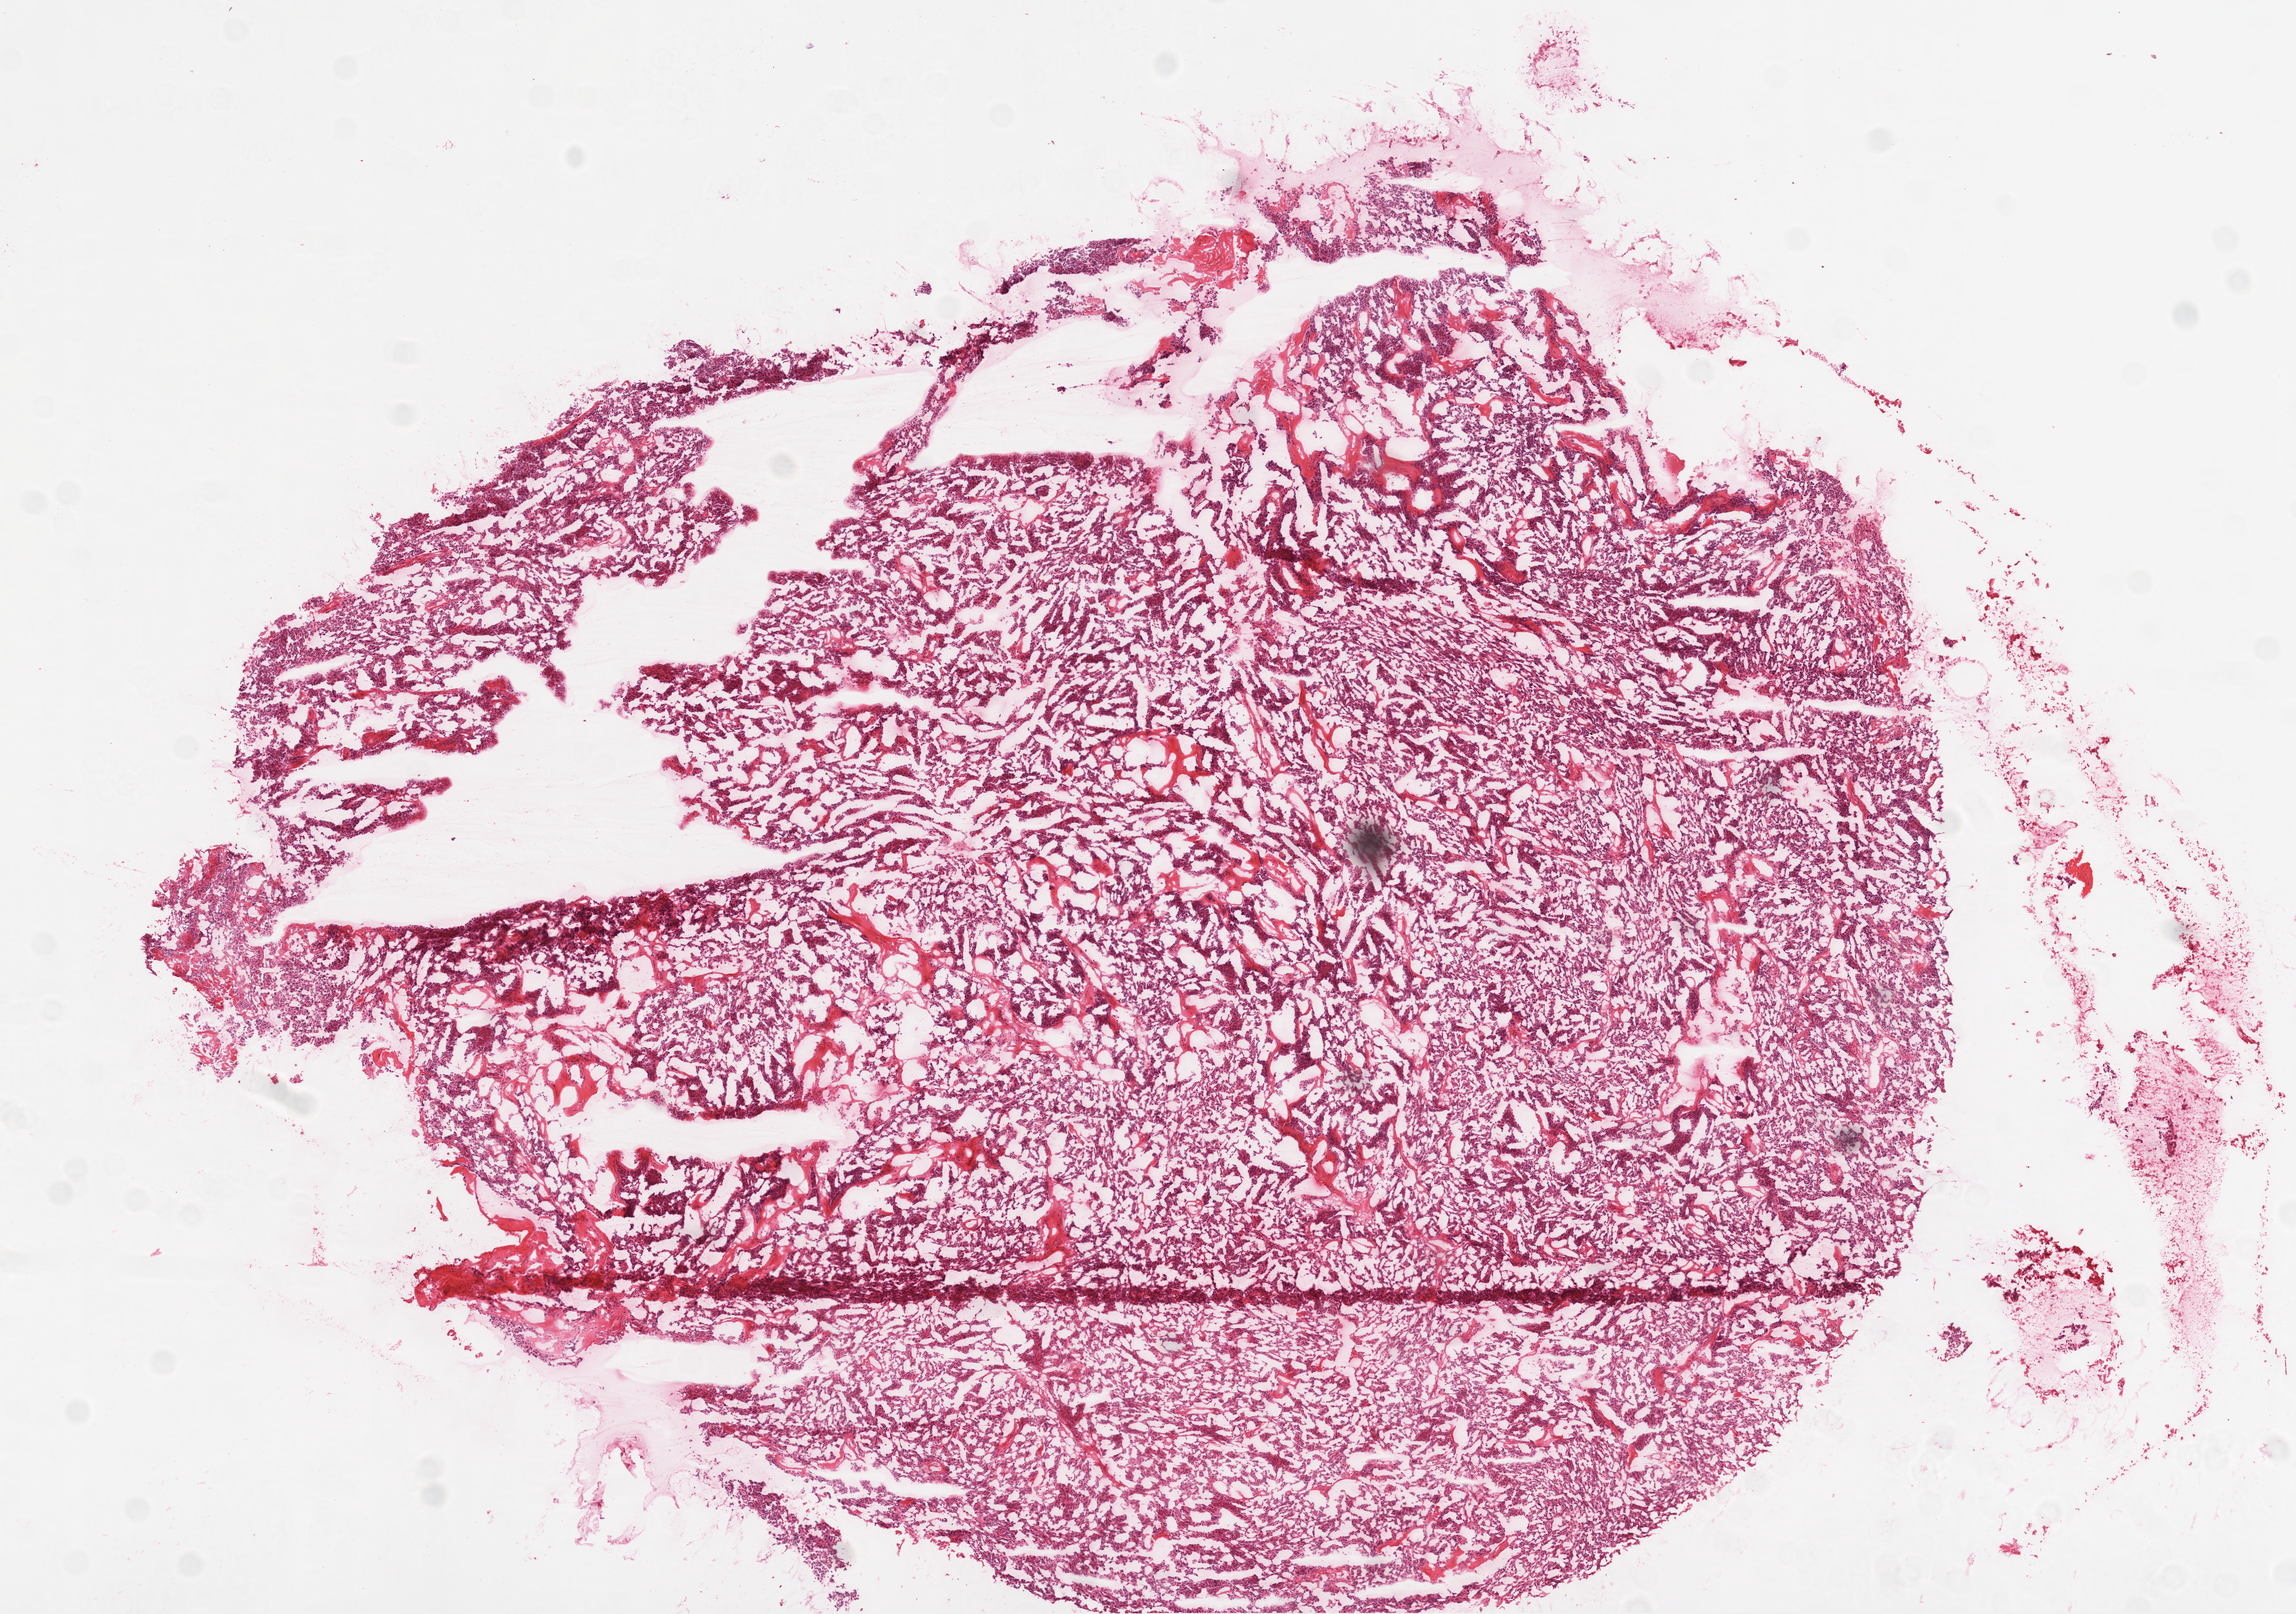
H&E-stained whole-slide image, shown as a low-resolution overview of the whole scanned area (about 8.0 x 5.6 mm, acquisition: 20x scan); frozen section from the top of the tissue portion; recurrent tumour sample from the ovary. Patient: female, age at initial diagnosis 61 years. Pathologist review of this section (percent, as recorded): tumour cells 95%, tumour nuclei 90%, normal cells 0%, stromal cells 5%, necrosis 0%.
This section: recurrent tumour. Patient diagnosis: Serous cystadenocarcinoma, NOS.